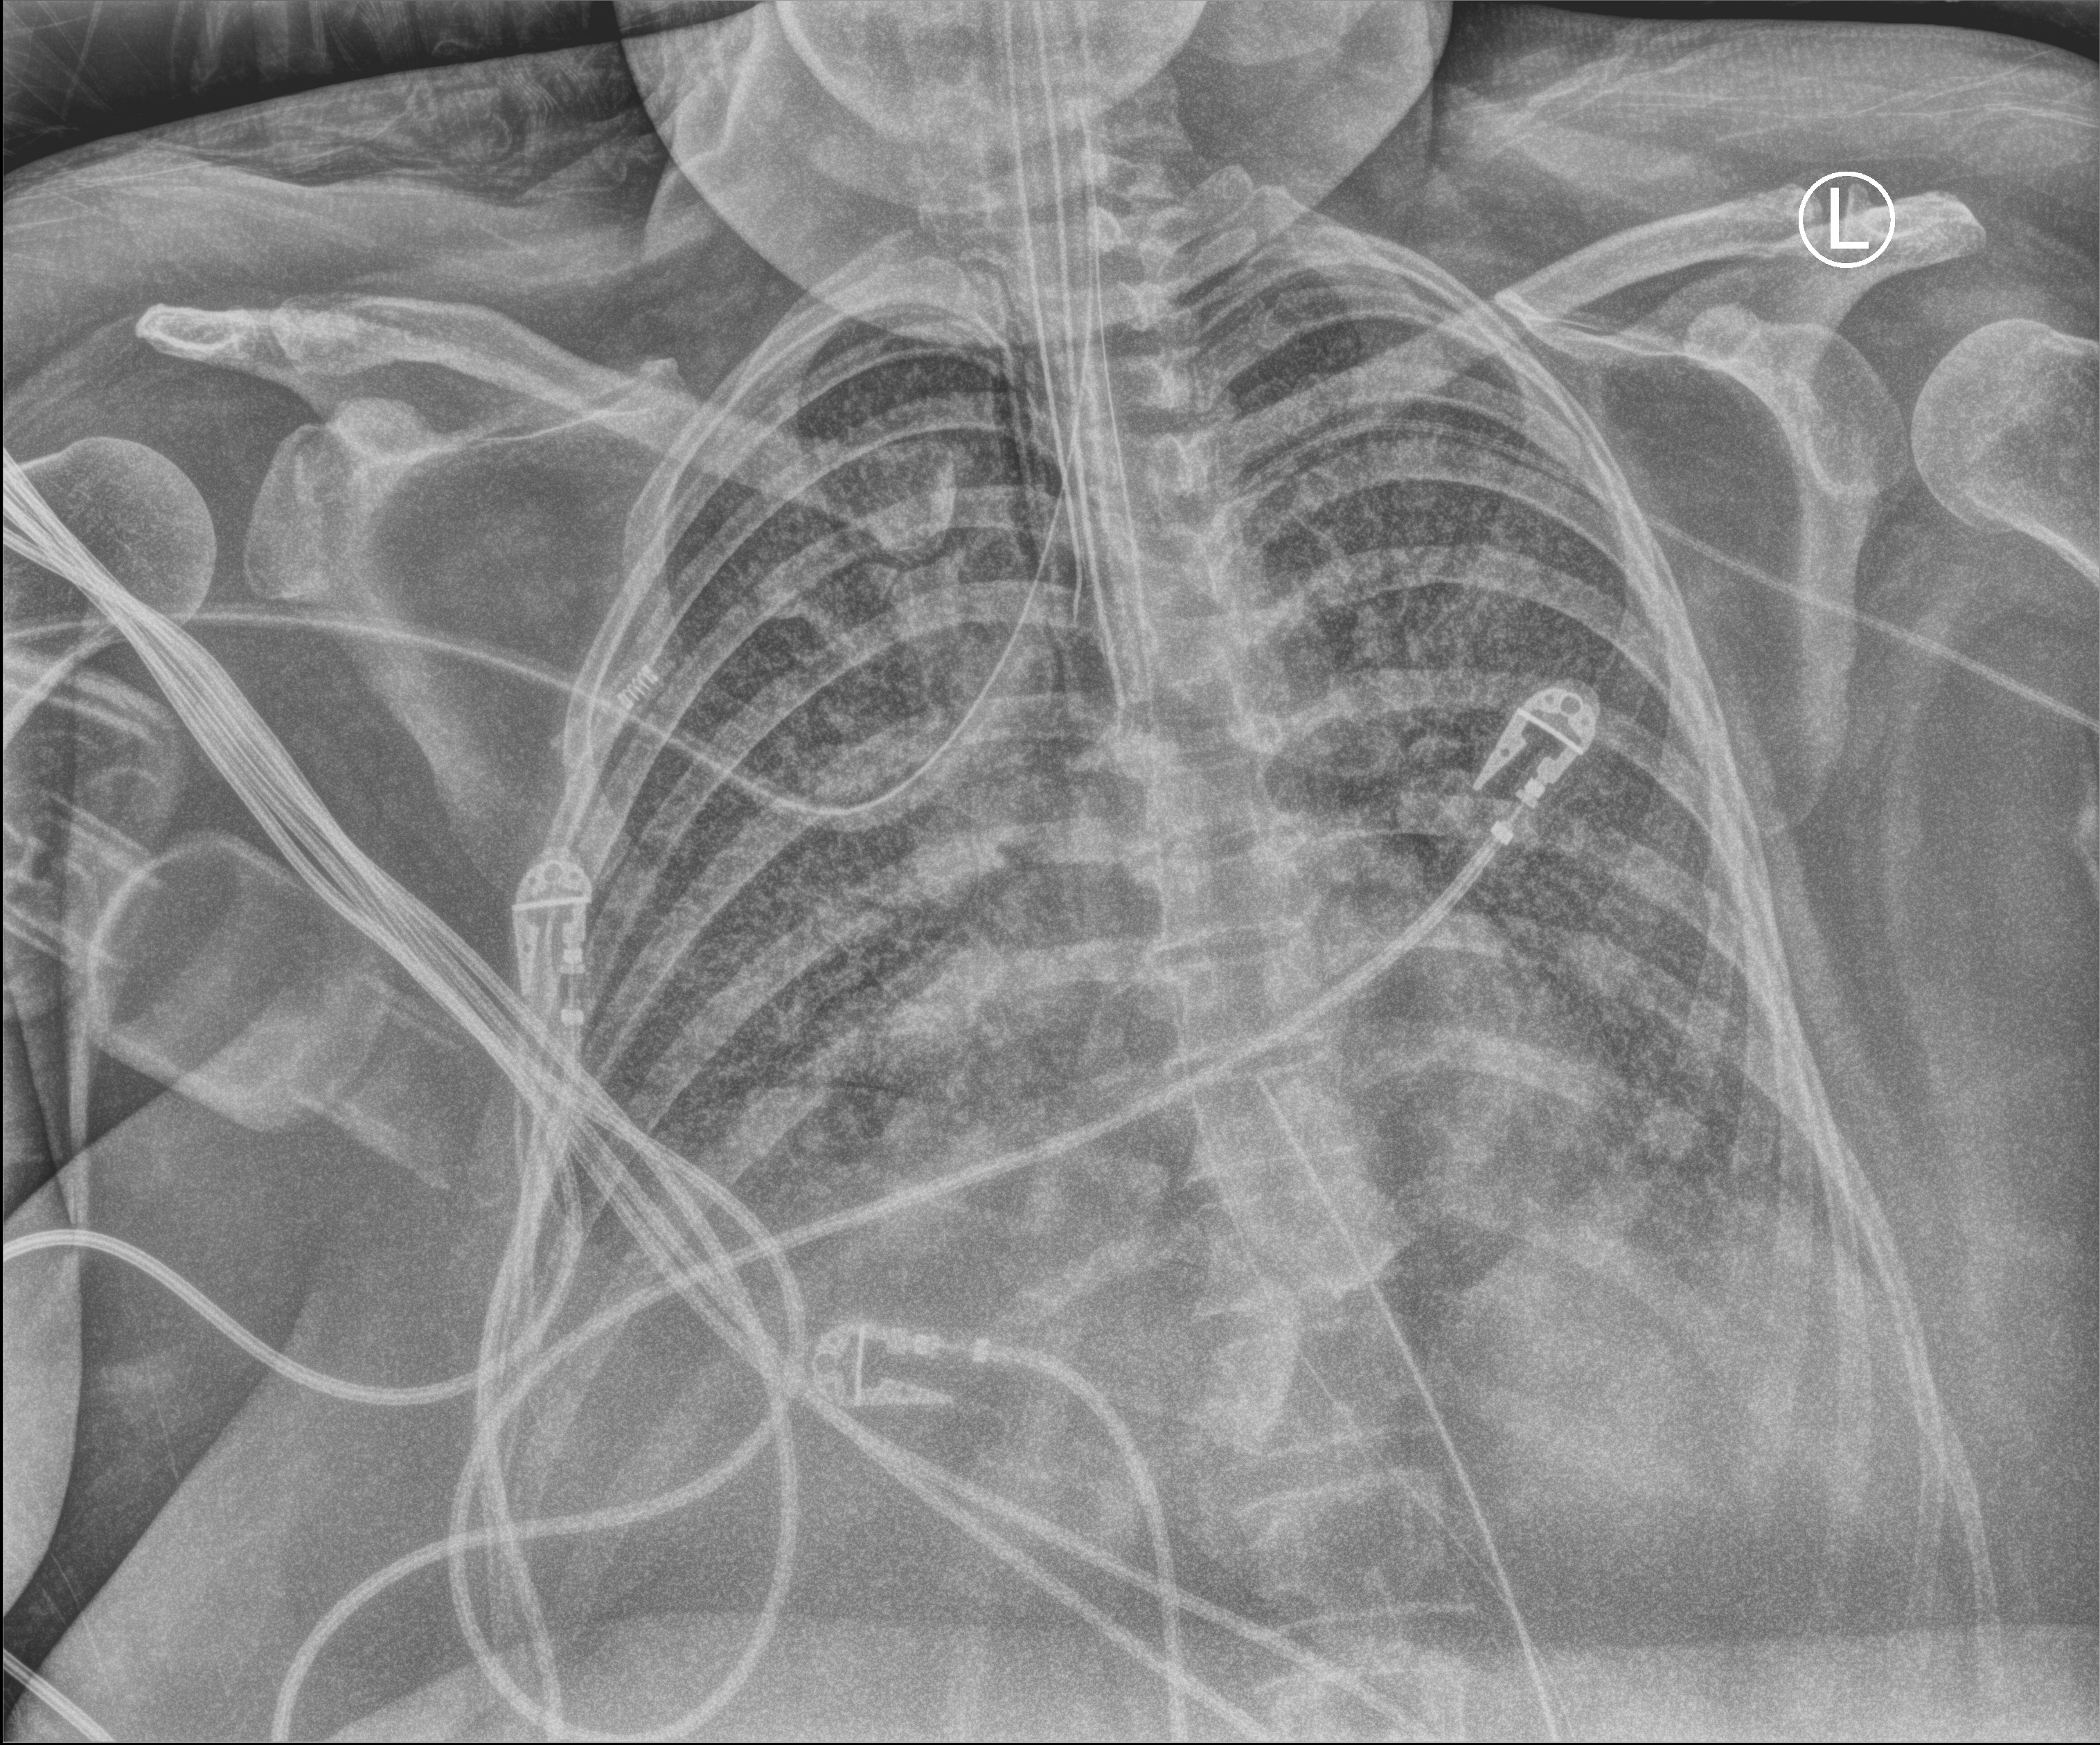
Chest X-ray (portable); anteroposterior (AP) projection. Female patient hospitalised with COVID-19, age 18–59 years.
Hospital-stay facts (about this admission, not read from this image; timing relative to this image not recorded): mechanically ventilated during this hospital stay: yes; length of hospital stay: 95 days.